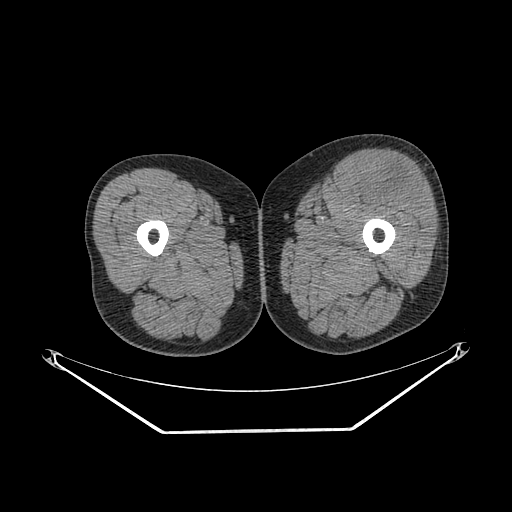
CT of an extremity soft-tissue mass (from a PET/CT study), one axial slice. Position 230 of 267 along the scan axis. Reconstruction kernel SOFT. Soft-tissue window (W 400 / L 40 HU). 3.75 mm slice thickness. 512 × 512 image matrix, field of view 500 × 500 mm. Male patient. Case-level facts recorded for this patient, not image findings: histological type: extraskeletal osteosarcoma; grade: high; site of the primary tumour: thigh.
Structures marked on this image (expert contour drawn on MRI and transferred to this co-registered scan by the dataset authors):
- gross tumour volume (mass): bounding box (x1, y1, x2, y2) in pixels: (358, 162, 428, 209)